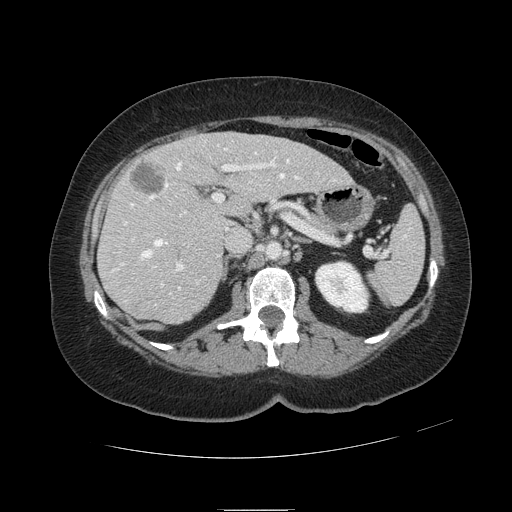
Contrast-enhanced abdominal CT, one axial slice; slice 61 of 121 in the series (ordered by position); soft-tissue window (W 400 / L 40 HU); 2.5 mm slice thickness; 512 × 512 image matrix, field of view 400 × 400 mm. Female patient, age 52 years. Case-level facts recorded for this patient, not image findings: diagnosis: colorectal cancer liver metastases, imaged before liver resection; multiple liver metastases: yes; largest metastasis: 6.3 cm.
Annotated regions visible in this slice (outlined manually by an expert reader):
- hepatic veins: box from (x=113, y=148) to (x=335, y=295) px
- liver: (x=99, y=132)–(x=351, y=323)
- planned liver remnant (the part of the liver to remain after resection): (x=168, y=133)–(x=351, y=216)
- portal vein (with intrahepatic branches): (x=124, y=152)–(x=276, y=271)
- liver metastasis: (x=131, y=164)–(x=166, y=195)